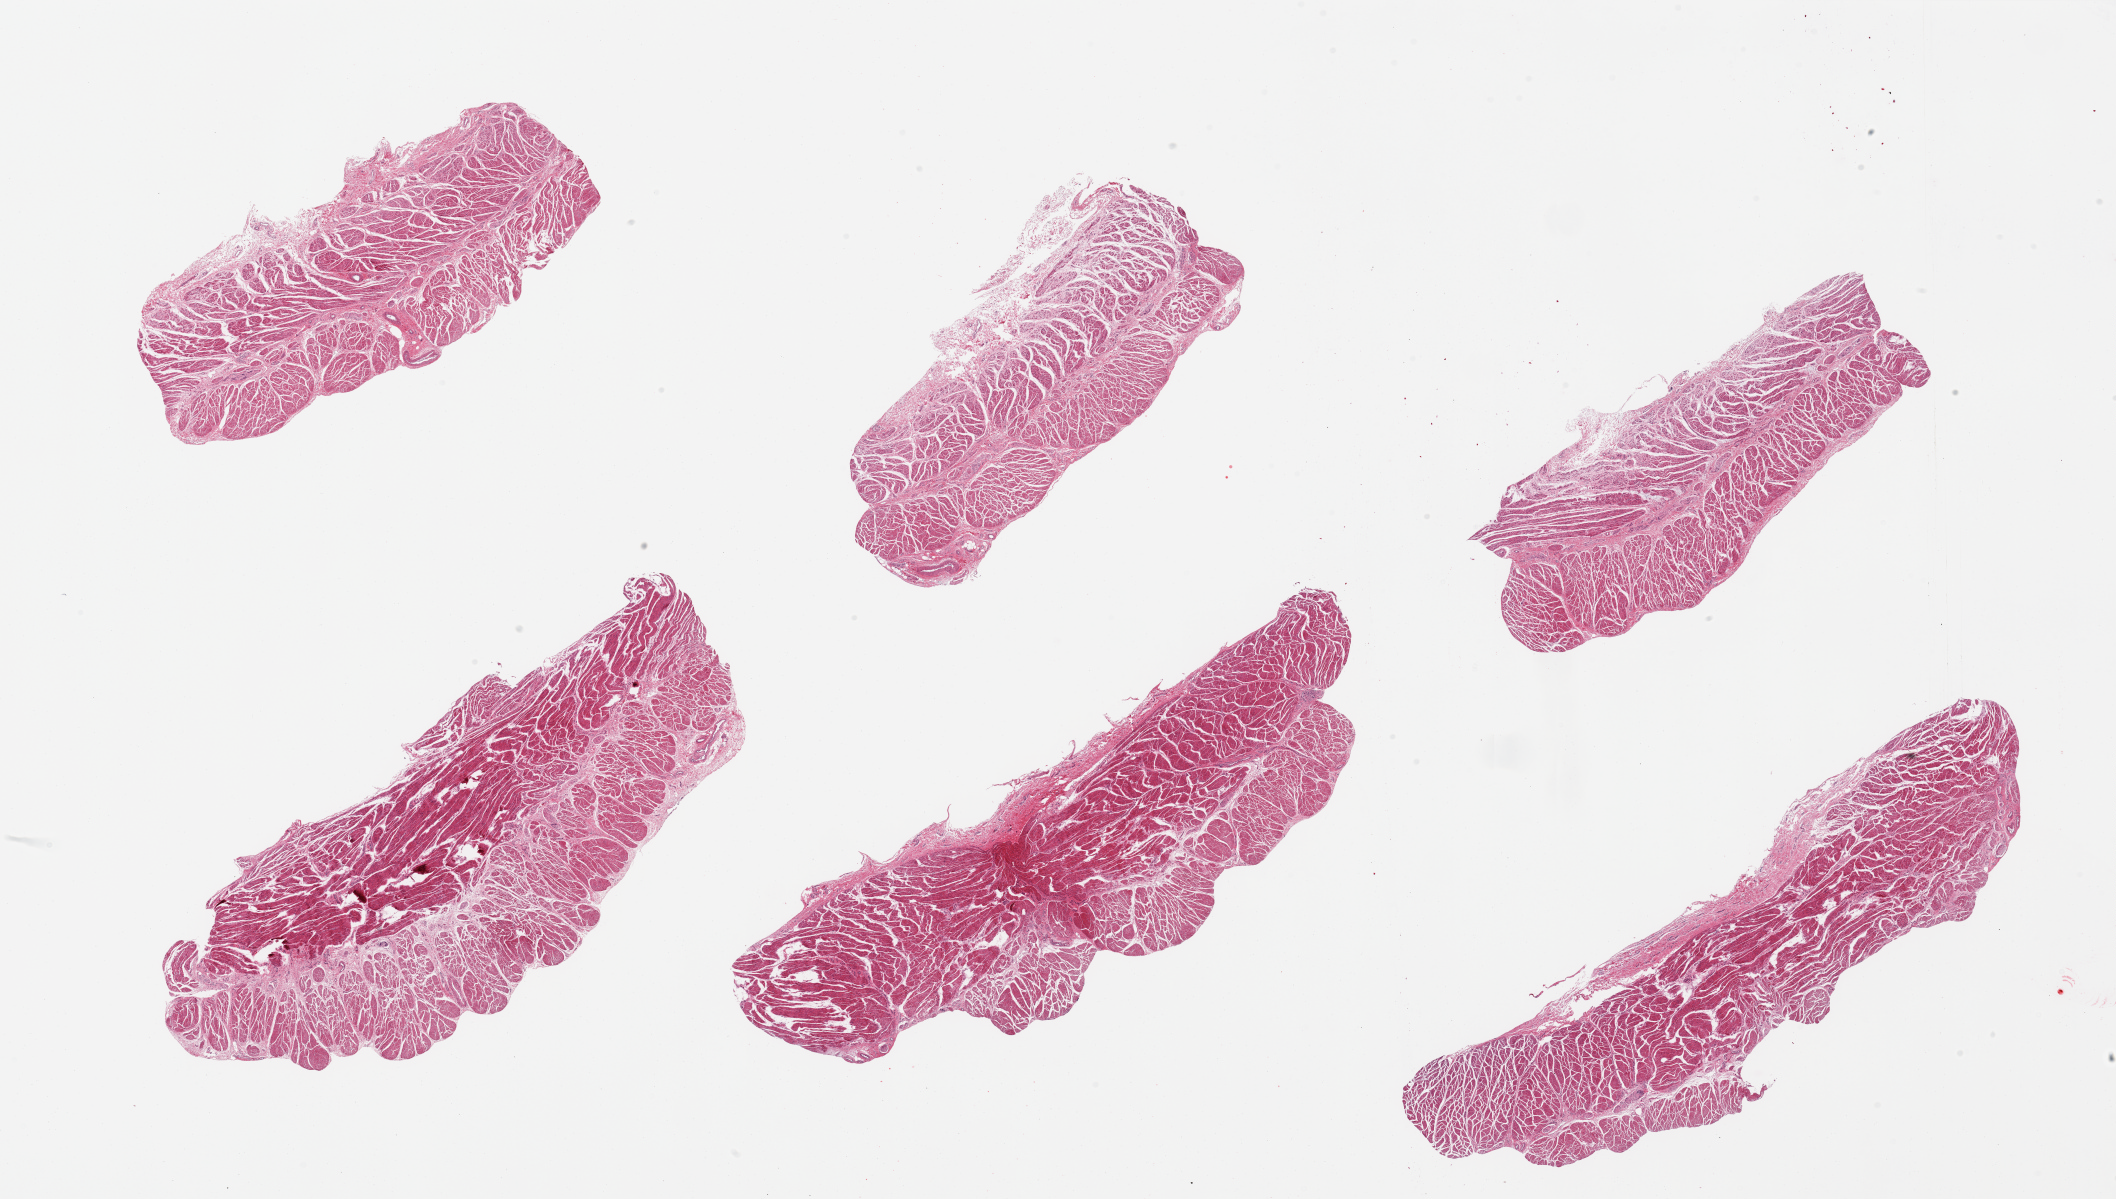
Whole-slide image, haematoxylin and eosin stain, brightfield — low-resolution overview of the scanned area, about 33.5 x 19.0 mm, PAXgene-fixed paraffin-embedded (PFPE) section, section of gastroesophageal junction (target tissue), tissue donor sample. Donor sex: male.
• pathologist's review note for this sample: 6 pieces